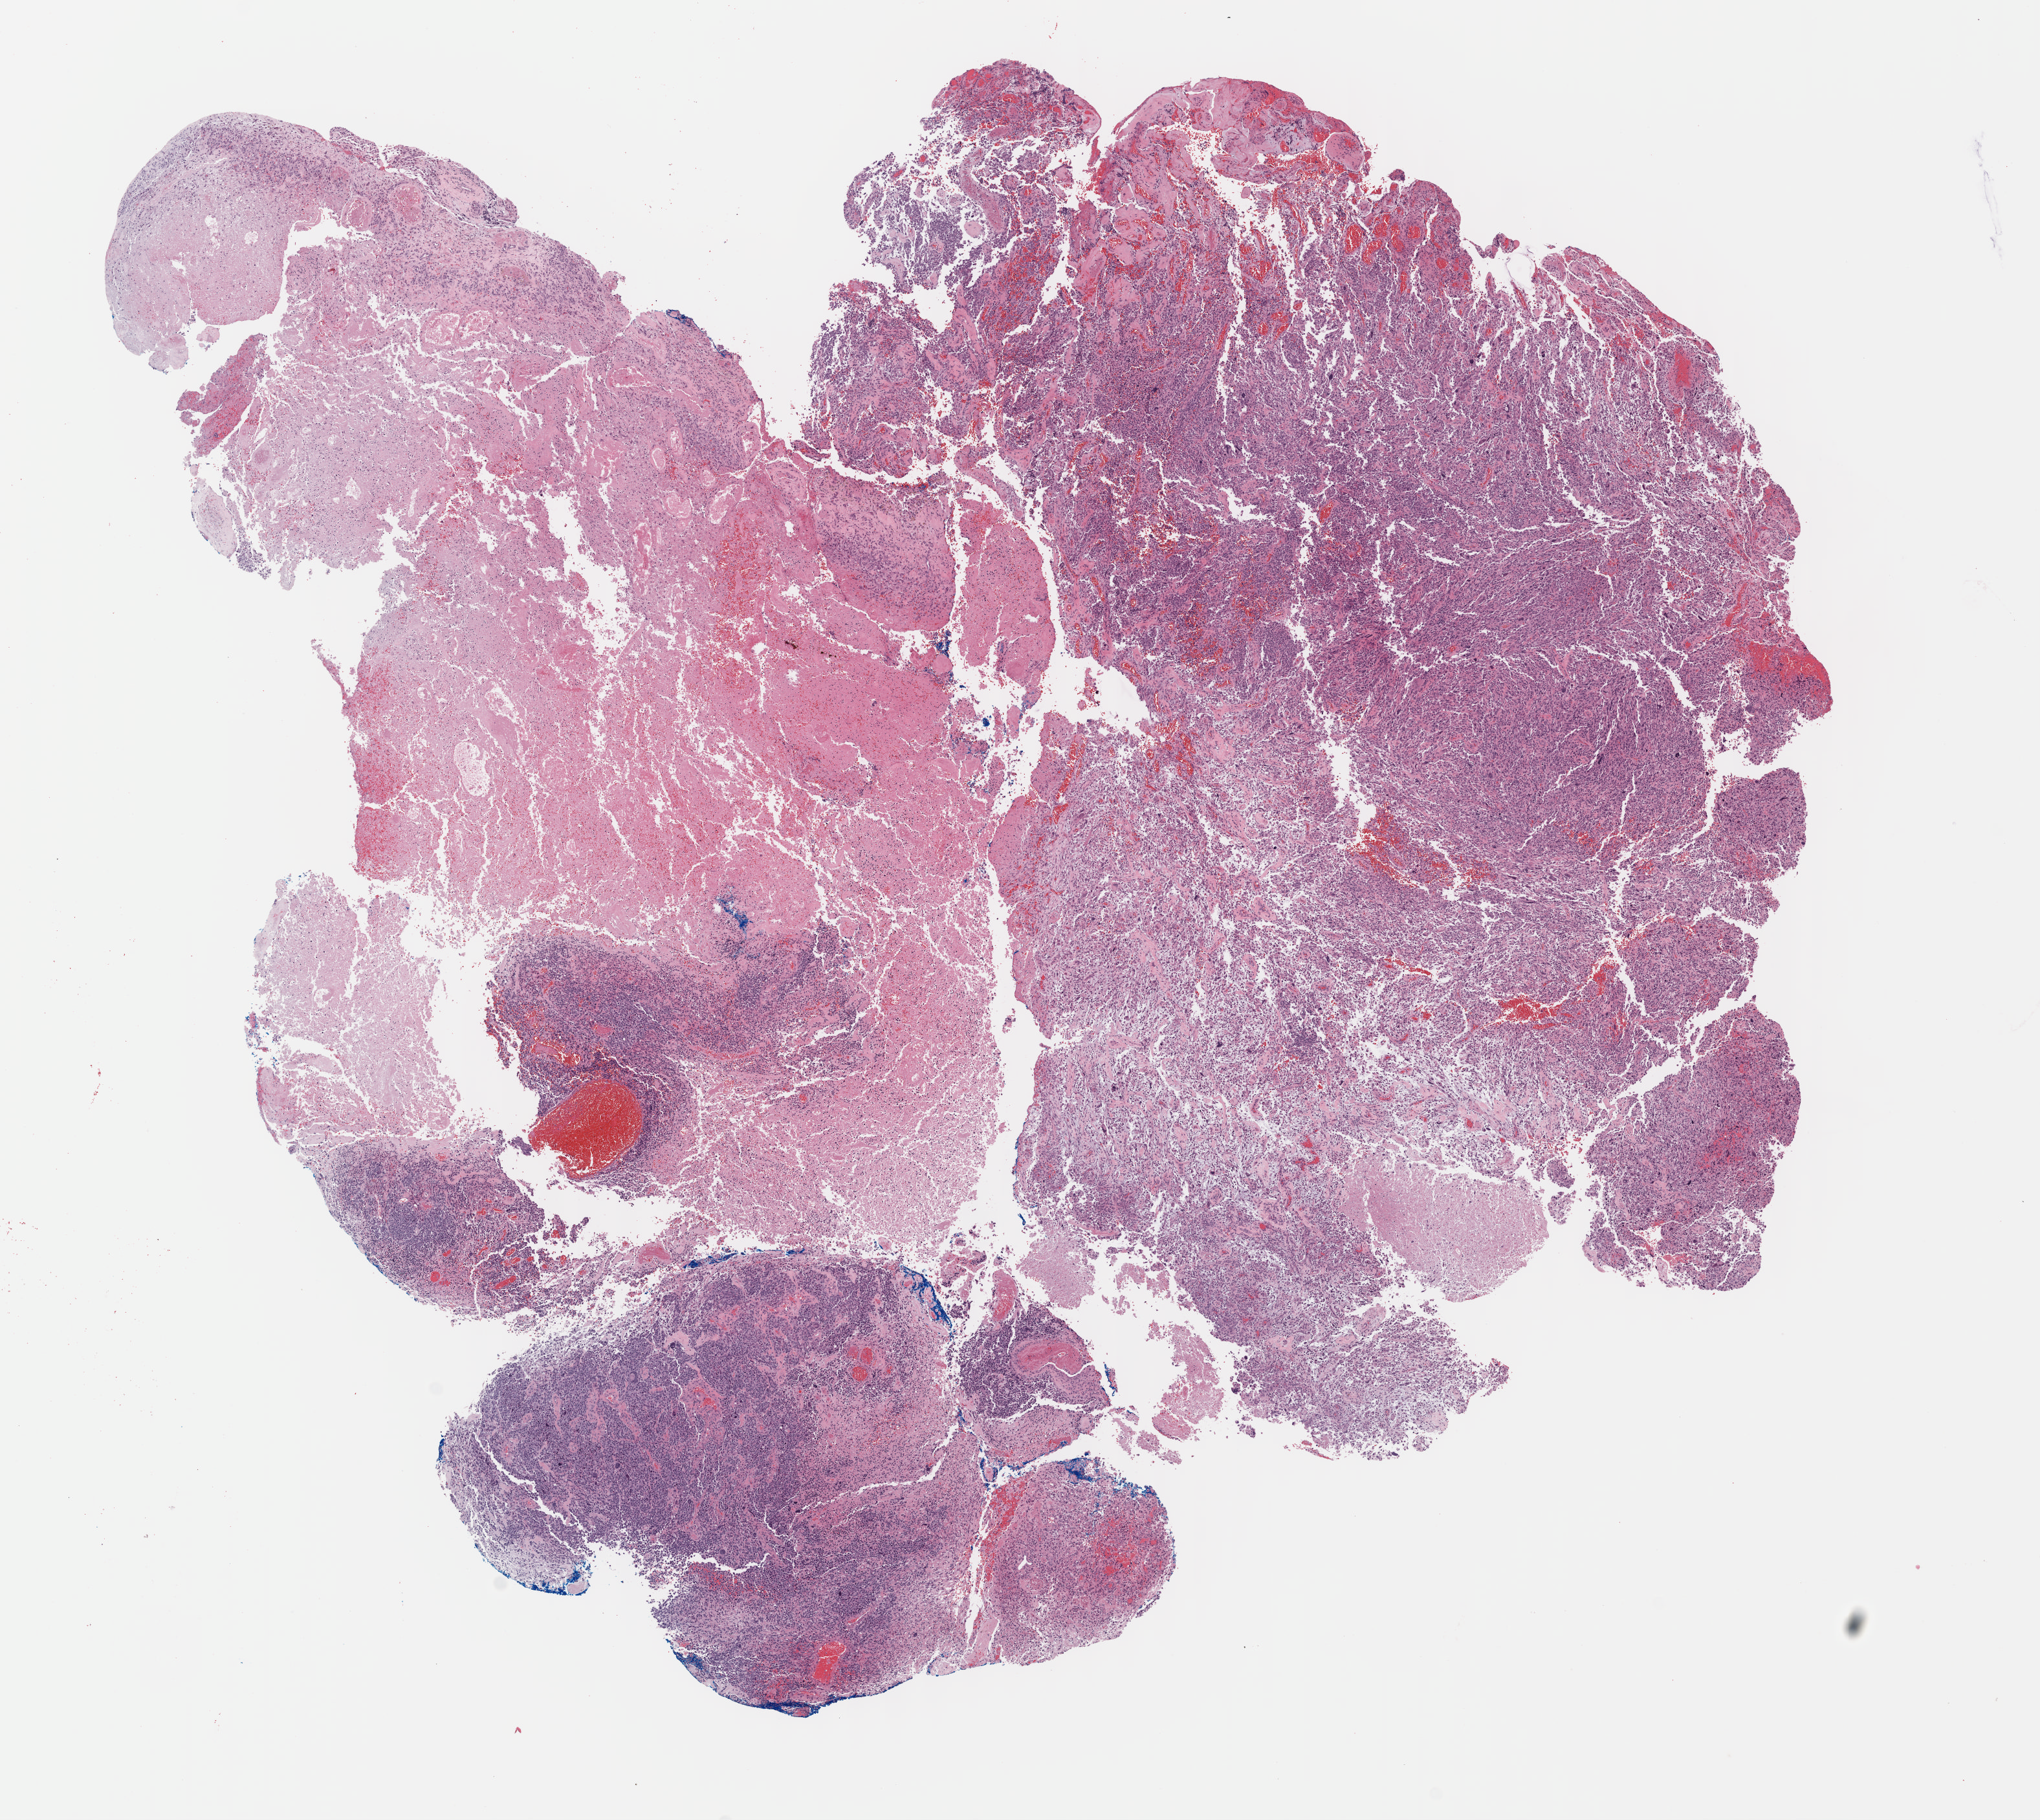
Digitized H&E tissue section (whole slide), a low-resolution overview of the entire scanned area, about 12.4 x 11.1 mm (from a 40x scan), formalin-fixed paraffin-embedded (FFPE) diagnostic section, brain, primary tumour sample. Patient: male, age at initial diagnosis 39 years.
* diagnosis: Glioblastoma